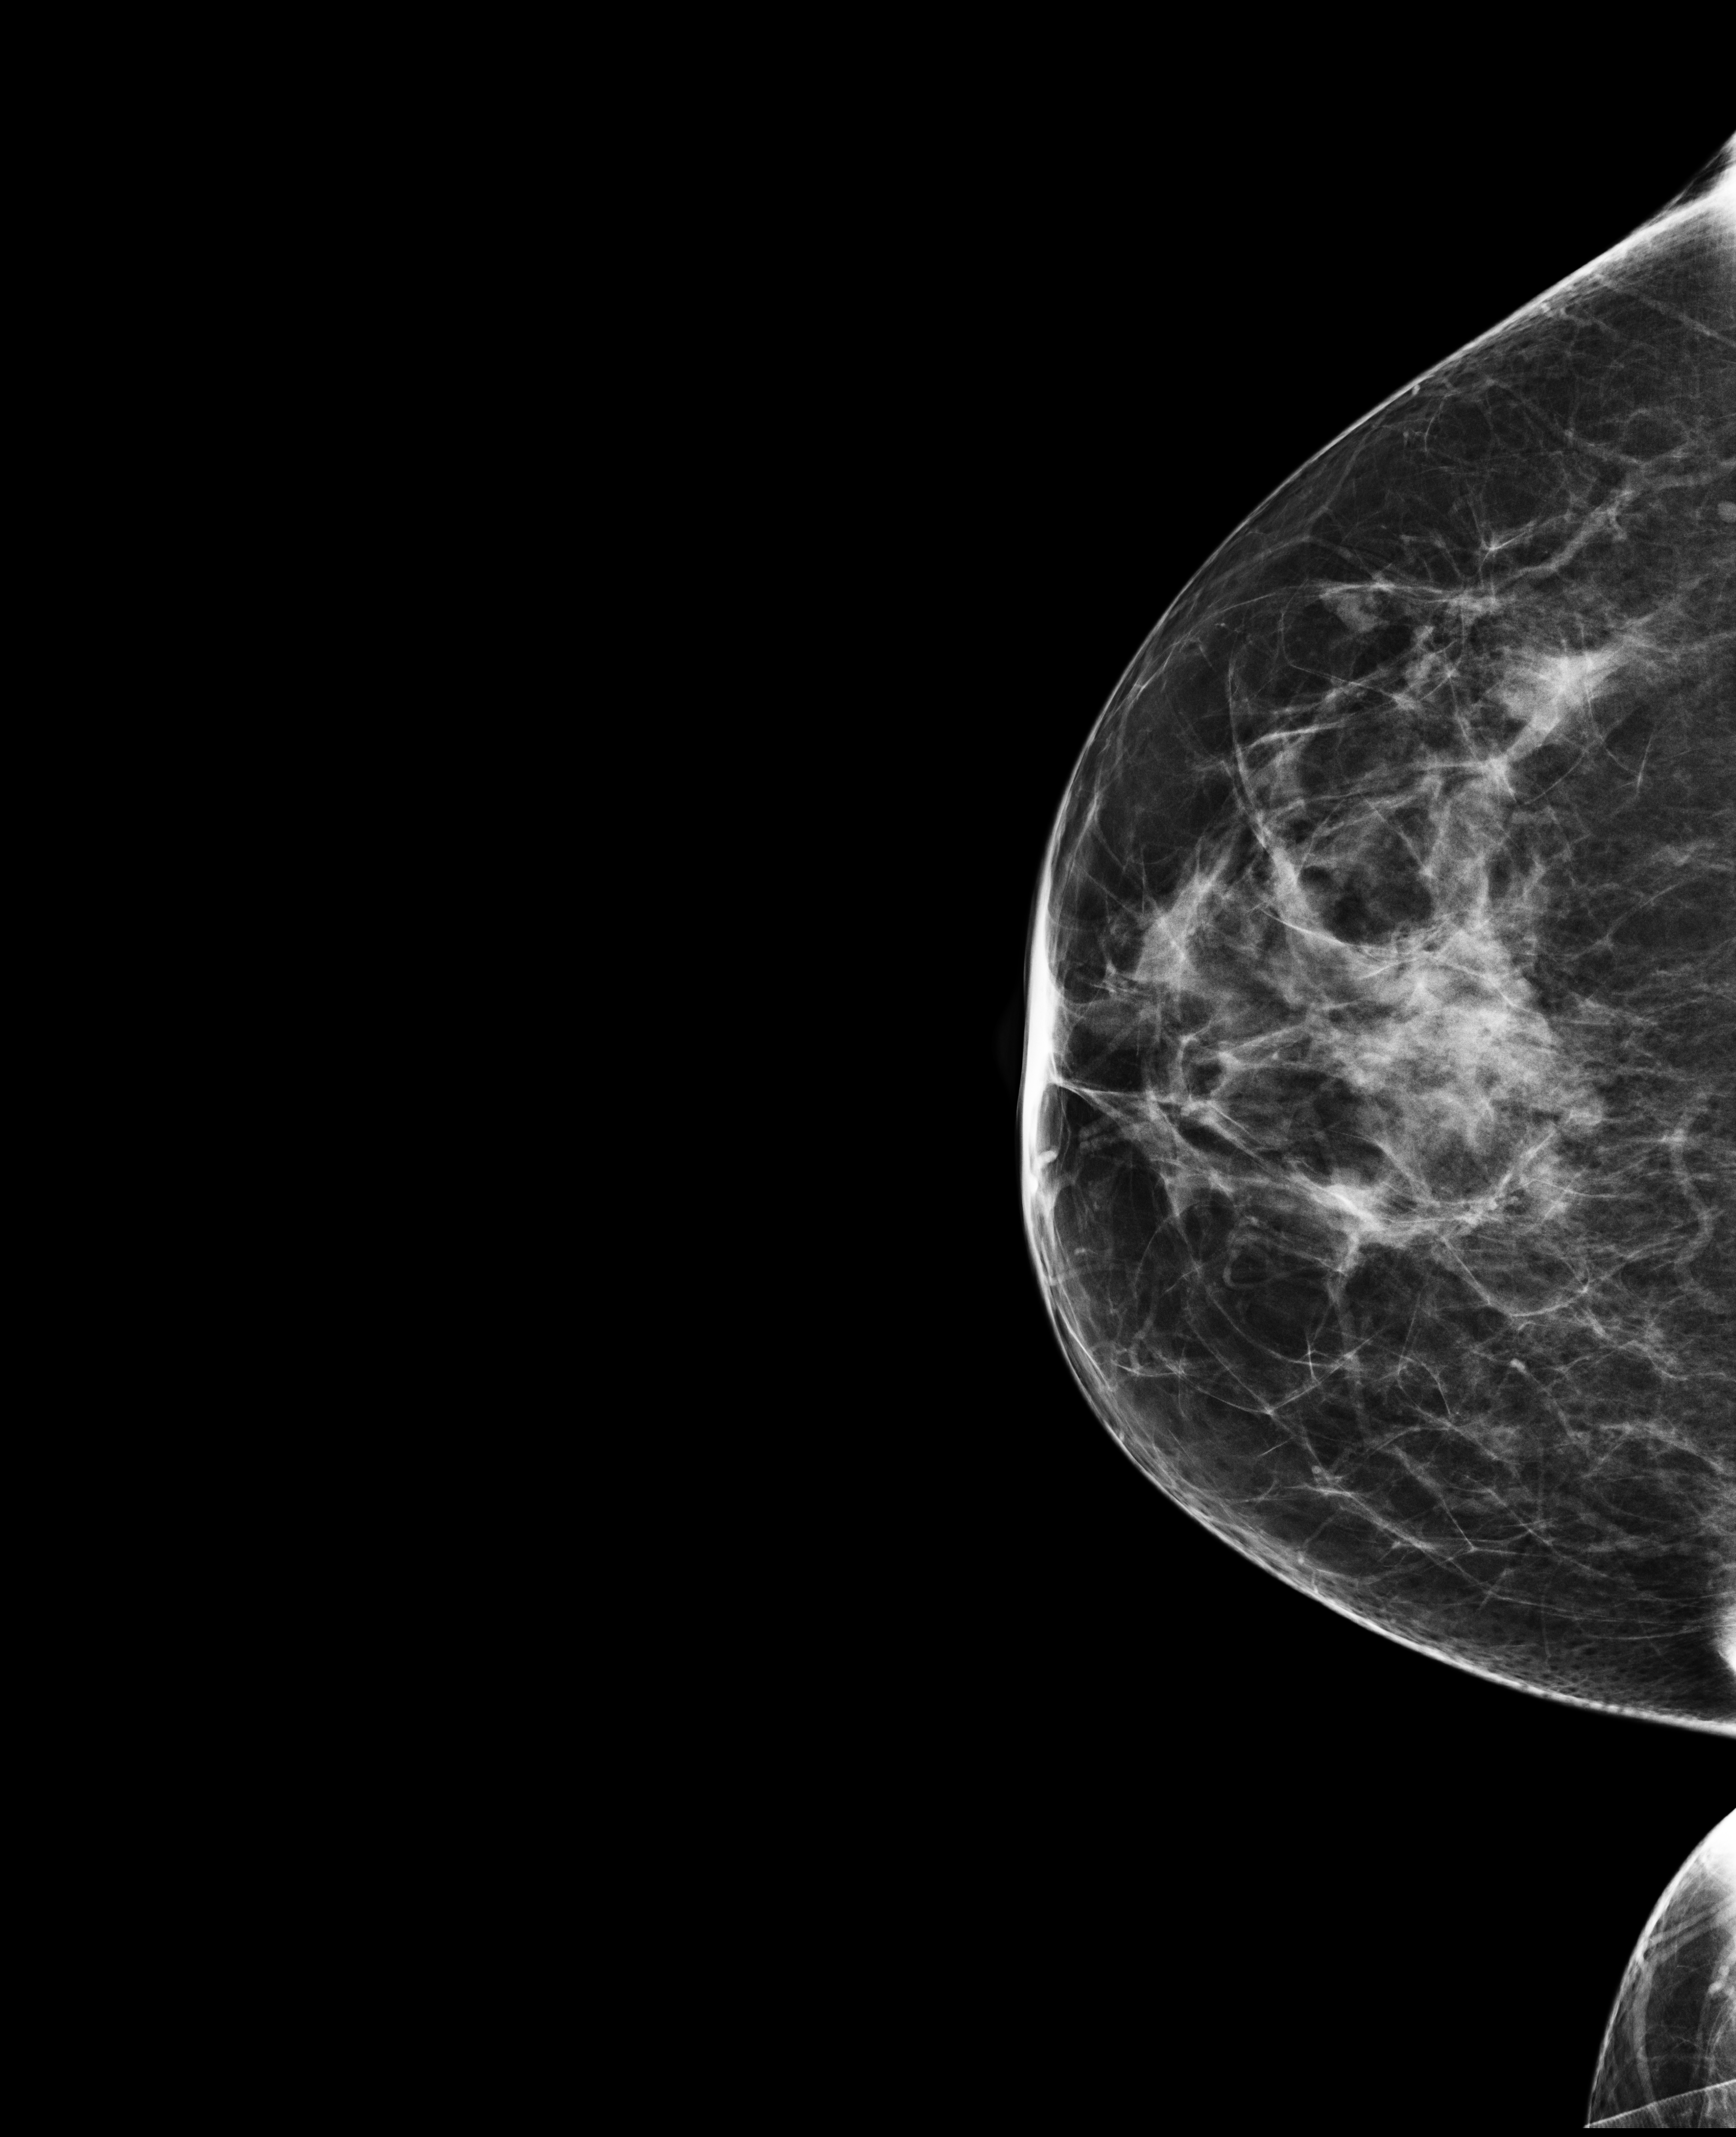
Digital mammogram (FFDM), right breast, CC view, screening examination. Patient aged 44 years (female).
Breast density at the screening exam (both breasts): heterogeneously dense (BI-RADS density category c). Final BI-RADS assessment for this screening round (tomosynthesis exam, both breasts): category 2. Recall: recalled for additional imaging after this screen.